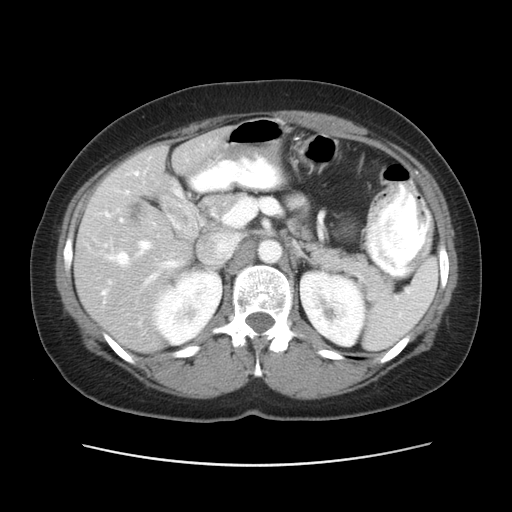
Contrast-enhanced abdominal CT, one axial slice. Position 30 of 52 along the scan axis. Reconstruction kernel STANDARD. 120 kVp. Intravenous contrast given. Soft-tissue window (W 400 / L 40 HU). 512 × 512 image matrix. Female patient, age 48 years. Case-level facts recorded for this patient, not image findings: diagnosis: colorectal cancer liver metastases, imaged before liver resection; multiple liver metastases: yes; largest metastasis: 4.5 cm; disease in both lobes: yes.
Structures marked on this image (manually delineated by an expert):
- hepatic veins: bounding box (x1, y1, x2, y2) in pixels: (102, 219, 179, 295)
- liver: (76, 131, 227, 351)
- planned liver remnant (the part of the liver to remain after resection): (173, 131, 227, 171)
- portal vein (with intrahepatic branches): (126, 172, 156, 282)
- liver metastasis: (129, 201, 144, 226)